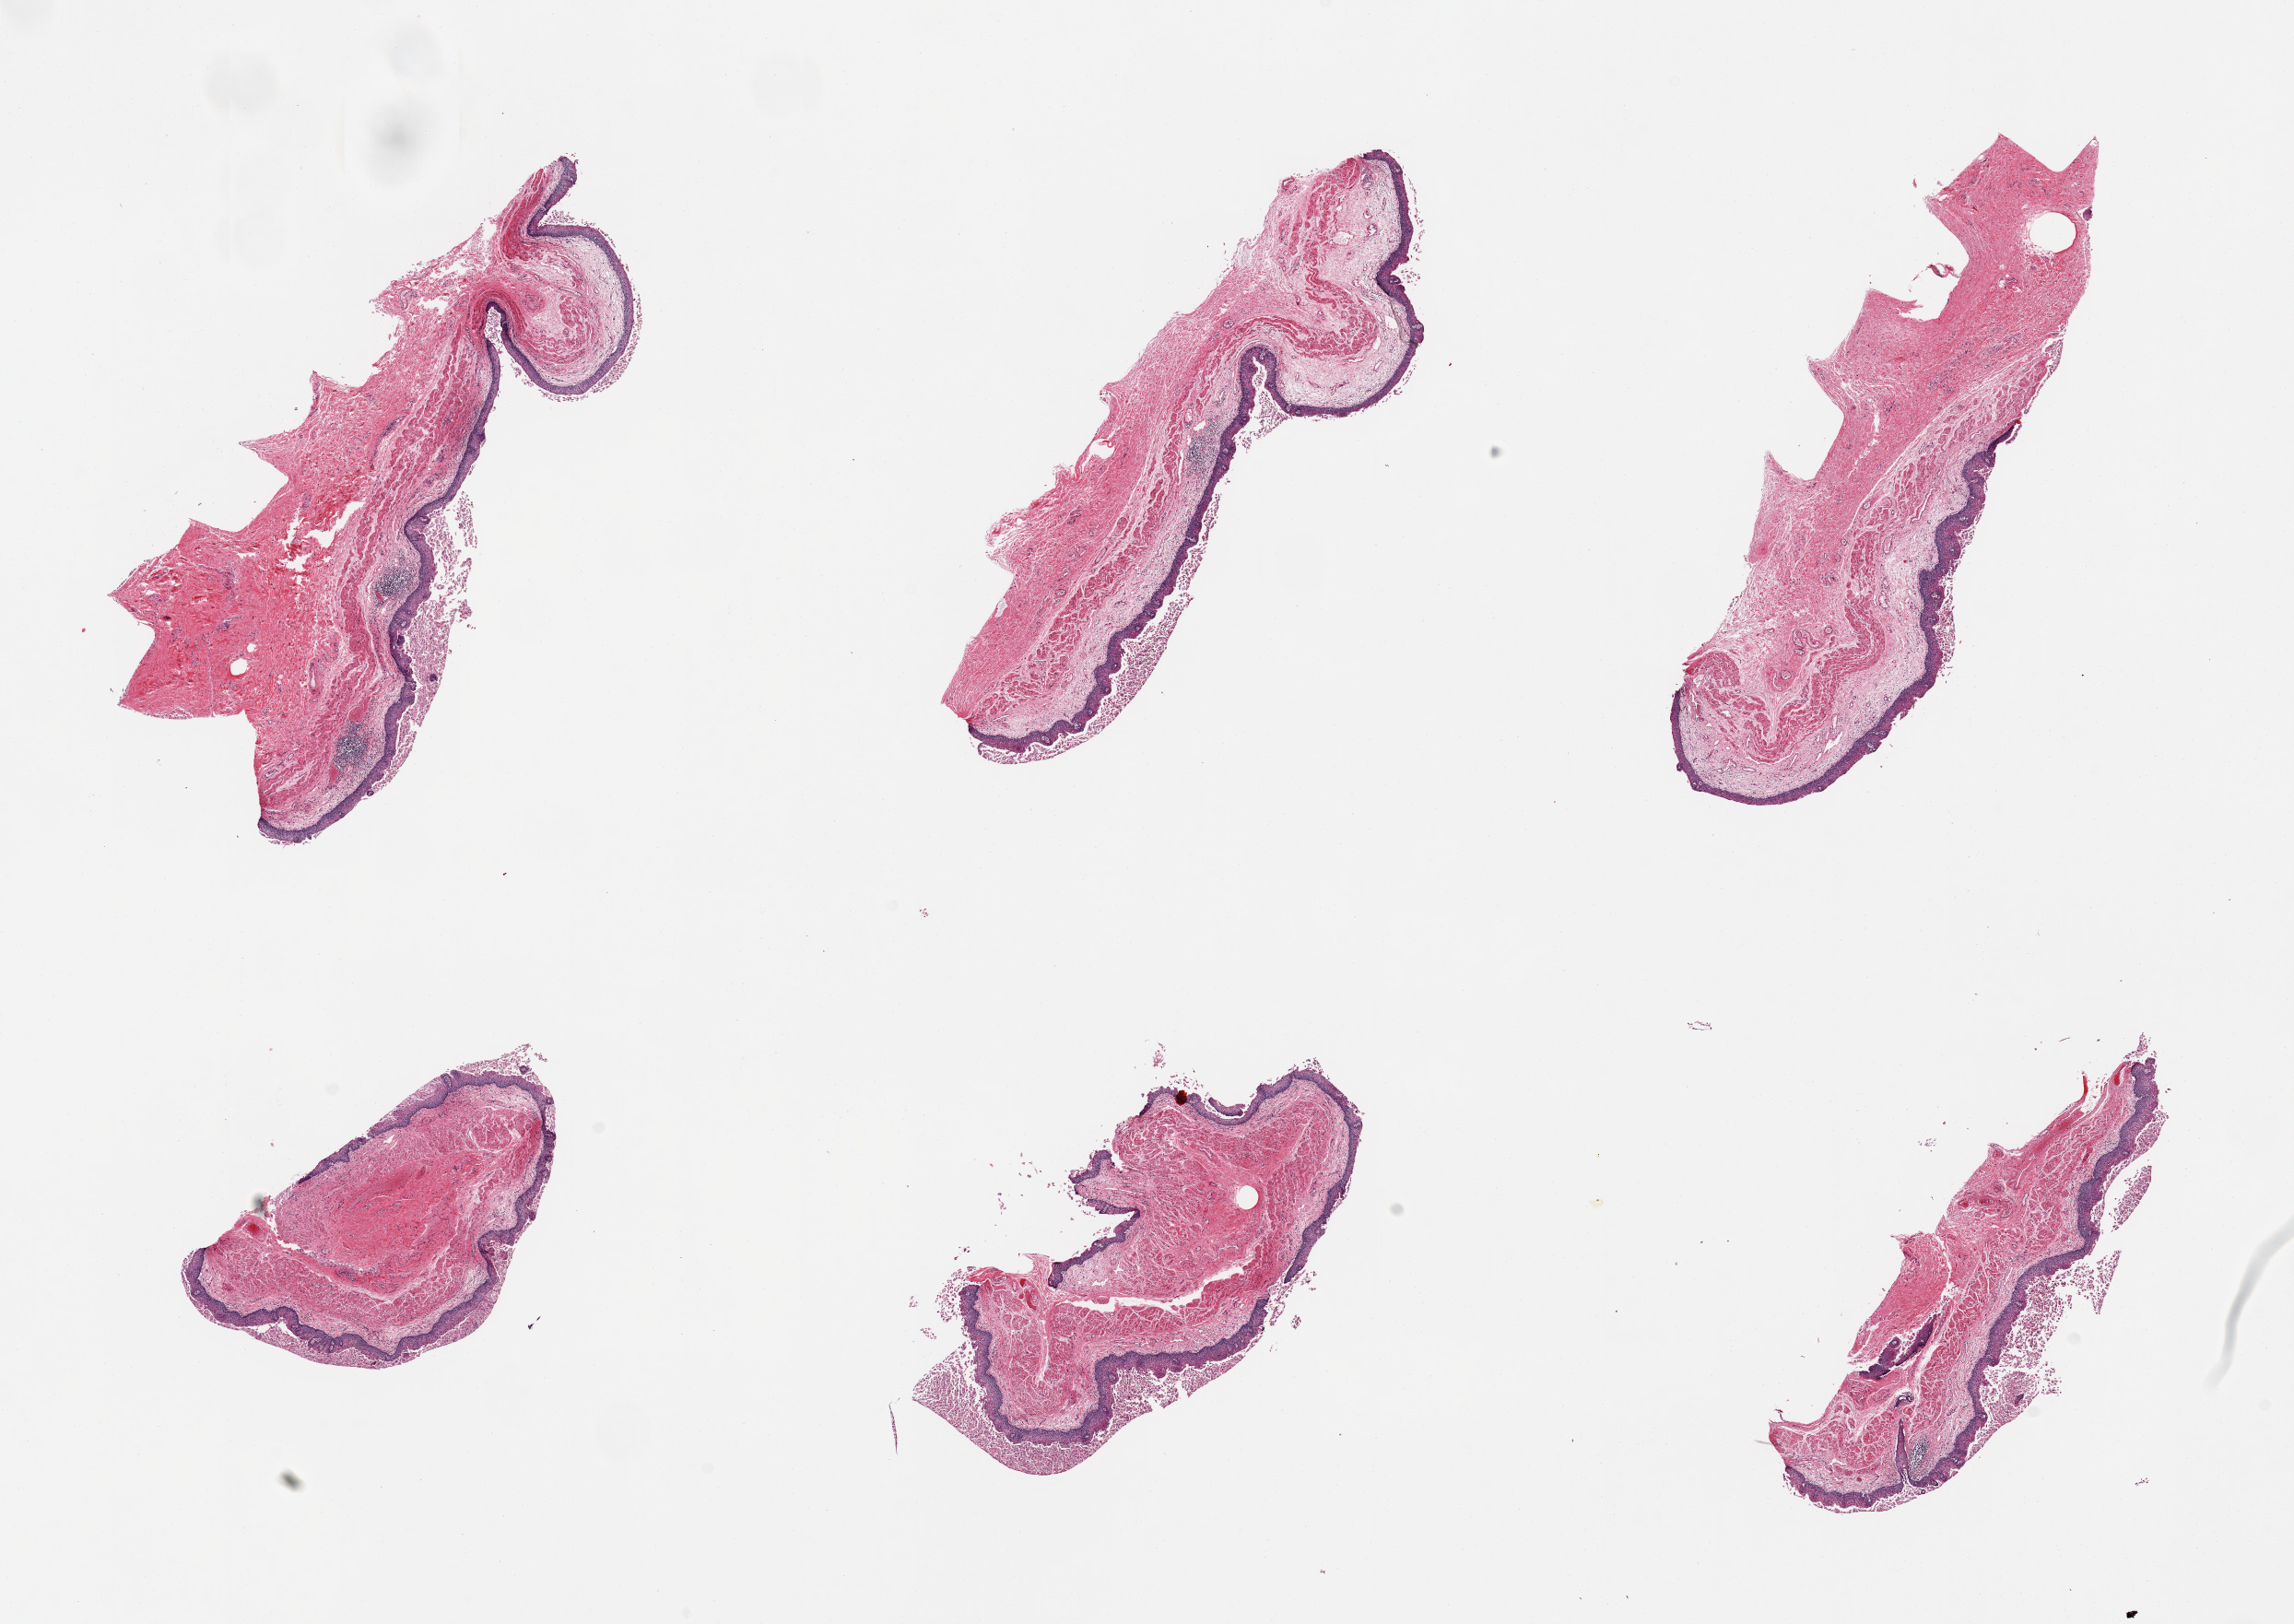
Digitized hematoxylin and eosin (H&E)-stained section, shown as a low-resolution overview of the whole scanned area (about 19.7 x 13.9 mm). PAXgene-fixed paraffin-embedded (PFPE) section. Target tissue: esophageal mucous membrane. Tissue donor sample.
Pathologist's review note for this sample: 6 pieces, squamous mucosa is ~0.1-0.2mm, moderate sloughing.